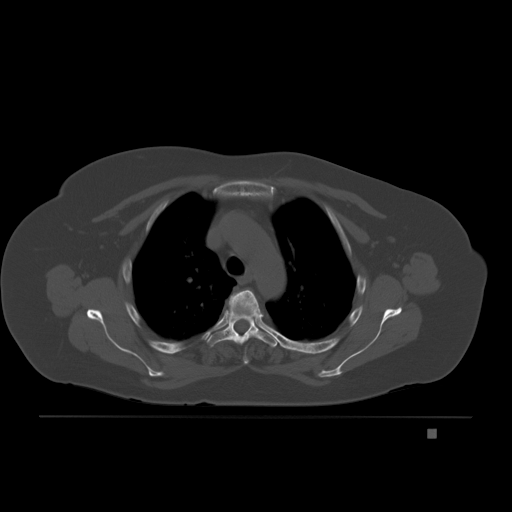
CT including the spine, one axial slice; position 155 of 221 along the scan axis; bone window (W 1800 / L 400 HU); 512 × 512 image matrix, field of view 474 × 474 mm. Female patient, age 63 years. Case-level facts recorded for this patient, not image findings: primary cancer: breast.
Outlined on this slice (semi-automatic segmentation, software-assisted and operator-edited):
- T3 vertebra: bounding box <229,290,257,363> (left, top, right, bottom; pixels)
- T4 vertebra: <207,312,278,348>